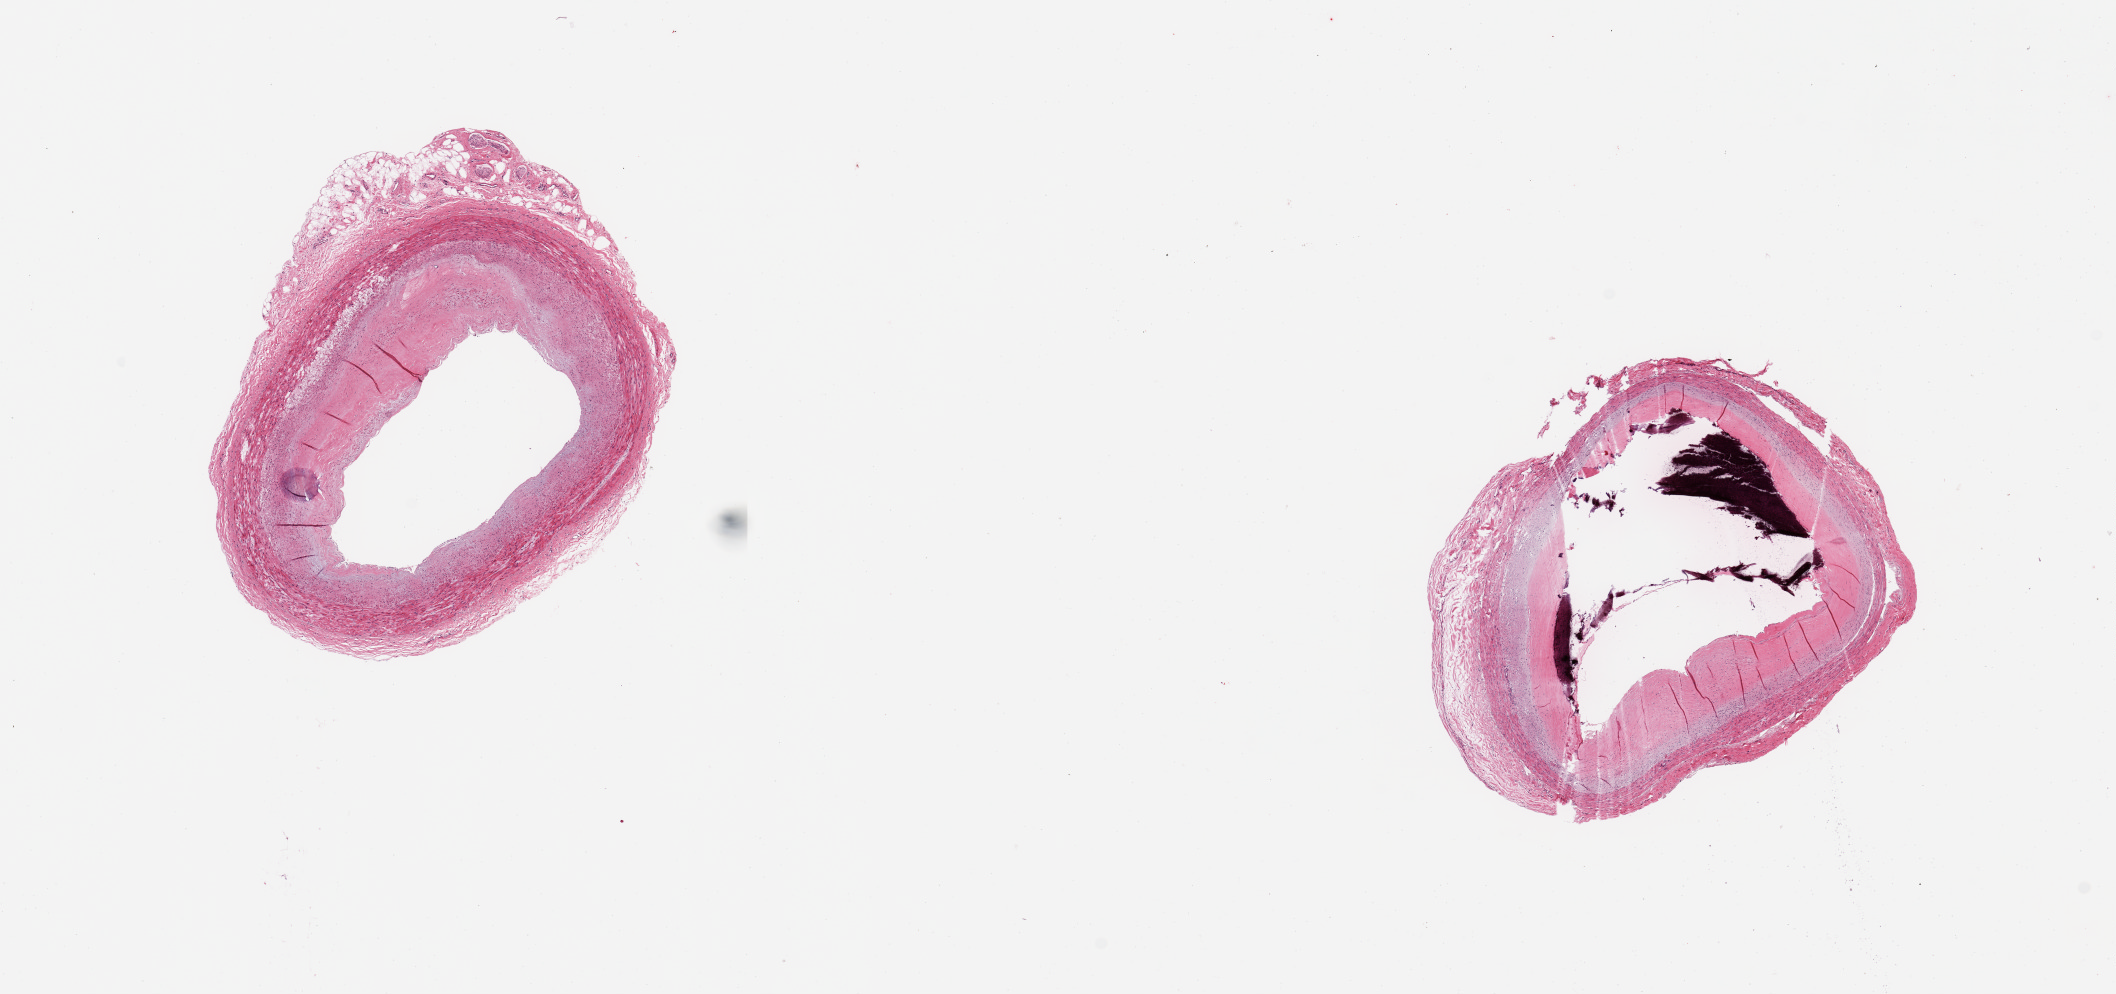
Whole-slide image, haematoxylin and eosin stain, shown as a low-resolution overview of the whole scanned area (about 16.7 x 7.9 mm, slide scanned at 20x); PAXgene-fixed, paraffin-embedded tissue; section of coronary artery (target tissue); donor tissue sample. Donor sex: male.
Reviewer comment on this tissue sample: 2 pieces, subtotally occlusive (~80%) calcifying atherosis.